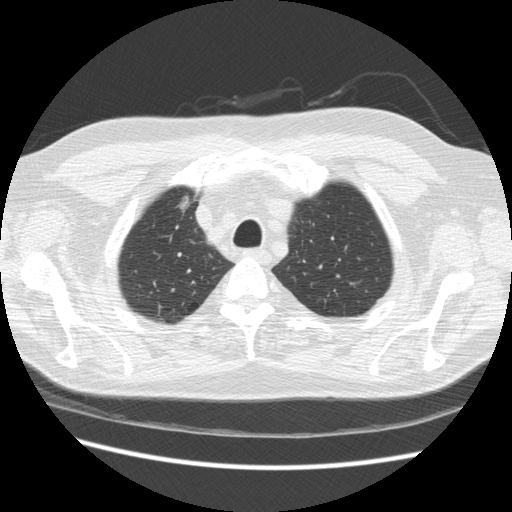
Low-dose screening chest CT, axial slice, third screening round (two years after baseline), lung window (W 1500 / L -600 HU), slice 42 of 234 in the series, 512 × 512 image matrix, field of view 360 × 360 mm. Male, age 66 years at enrolment. Former smoker at enrolment.
• Expert-annotated lung lesion, bounding box <167,187,207,222> (left, top, right, bottom; pixels).
• Screening reader's record for this exam: no non-calcified nodule ≥4 mm recorded.
• Participant outcome: lung cancer diagnosed 229 days after this screen — bronchiolo-alveolar adenocarcinoma, NOS, right upper lobe, moderately differentiated (G2), stage IA (AJCC 6th edition), 12 mm at pathology.